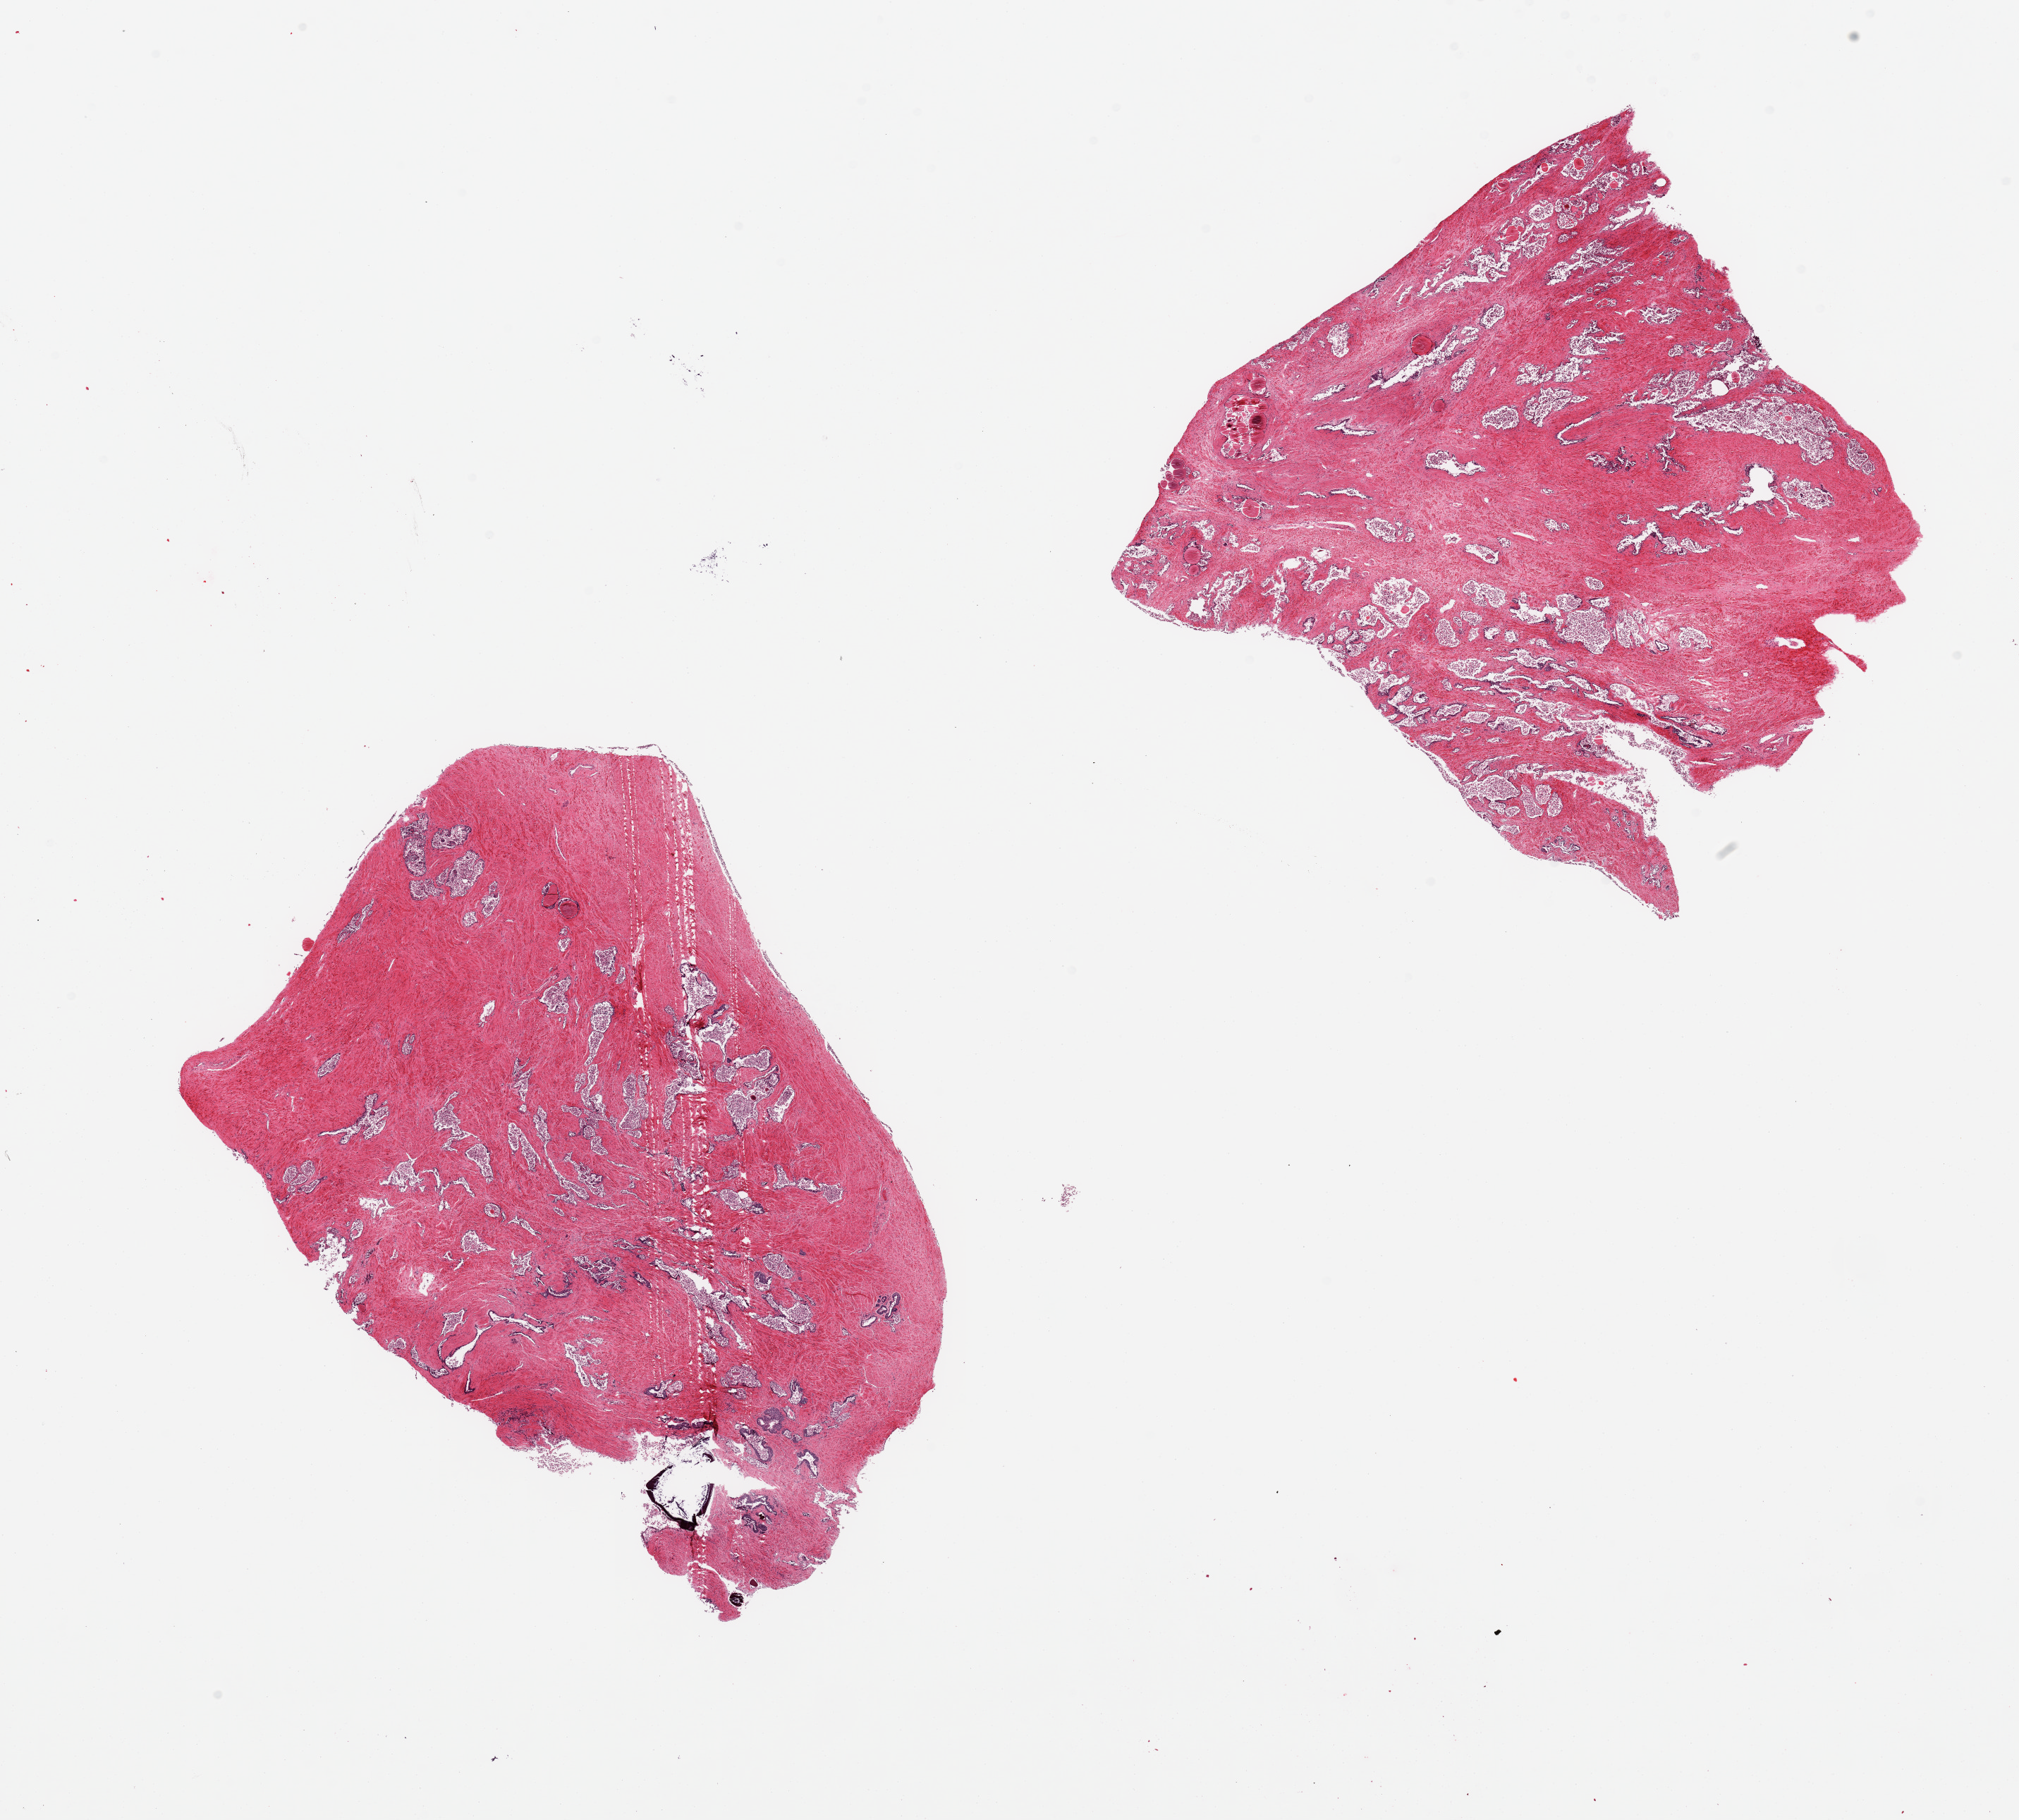
Whole-slide image, hematoxylin and eosin (H&E) stain, low-resolution overview of the scanned area, about 22.6 x 20.4 mm; PAXgene-fixed paraffin-embedded (PFPE) section; sampled site (target tissue): prostate; donor tissue sample. Donor: male.
- pathologist's review note for this sample: 2 pieces; glands autolyzed [3], stroma intact [1]